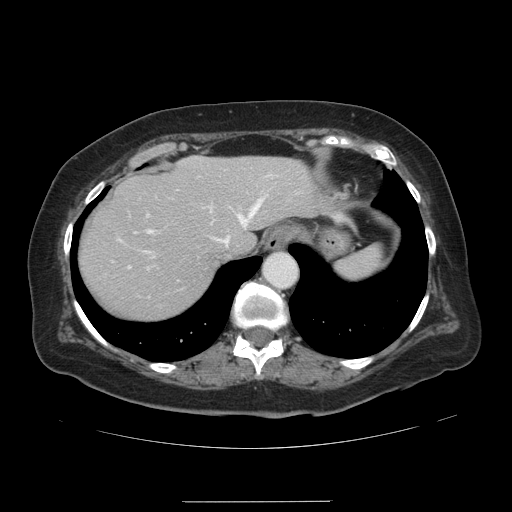
Contrast-enhanced abdominal CT, one axial slice. Slice 110 of 141 in the series (ordered by position). Soft-tissue window (W 400 / L 40 HU). 2.5 mm slice thickness. 512 × 512 image matrix, field of view 393 × 393 mm. Female patient, age 74 years. From the clinical record (not read from this slice): diagnosis: colorectal cancer liver metastases, imaged before liver resection; multiple liver metastases: yes; largest metastasis: 7 cm; disease in both lobes: yes.
Structures marked on this image (expert manual segmentation):
- hepatic veins: bounding box (x1, y1, x2, y2) in pixels: (143, 189, 271, 258)
- liver: (79, 156, 327, 318)
- planned liver remnant (the part of the liver to remain after resection): (79, 156, 327, 318)
- portal vein (with intrahepatic branches): (128, 208, 253, 267)